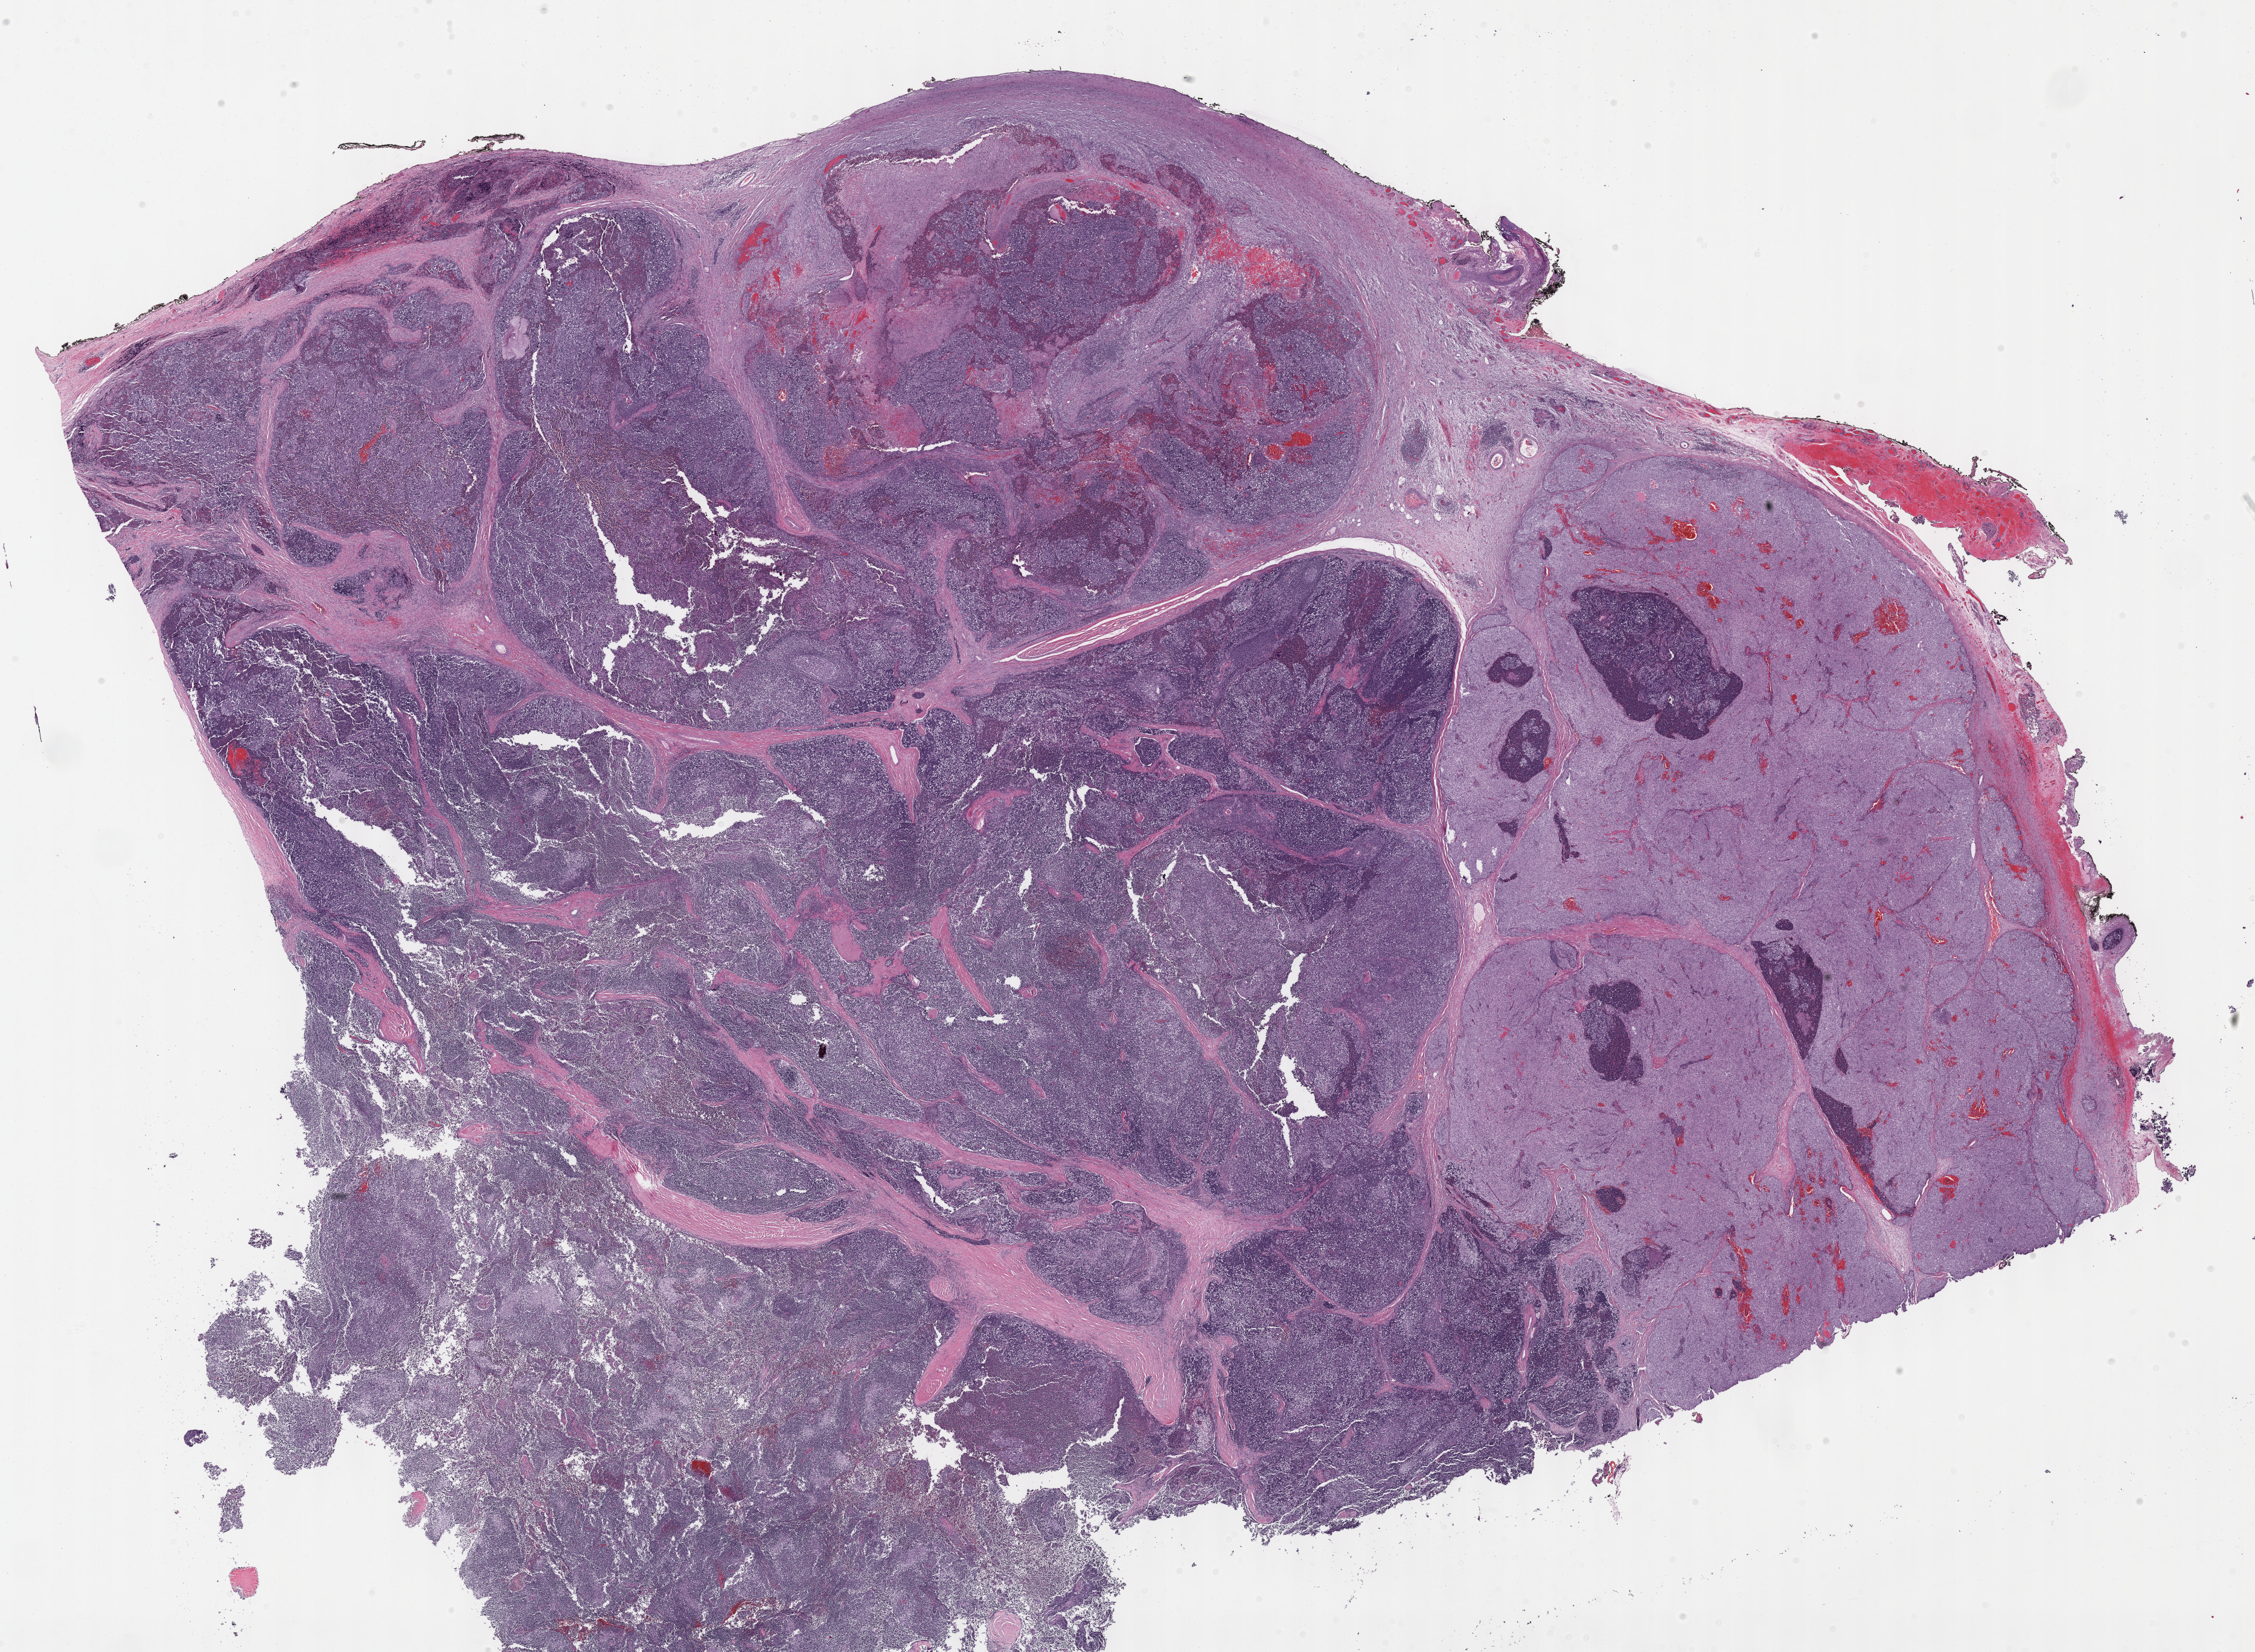
Digitized H&E-stained tissue section (whole slide), whole scanned area (about 30.2 x 22.1 mm) shown as a low-resolution overview; formalin-fixed paraffin-embedded (FFPE) diagnostic section; thymus, primary tumour sample. Male, age 42 years at initial diagnosis.
• pathologic diagnosis: Thymoma, type B2, malignant (anterior mediastinum)